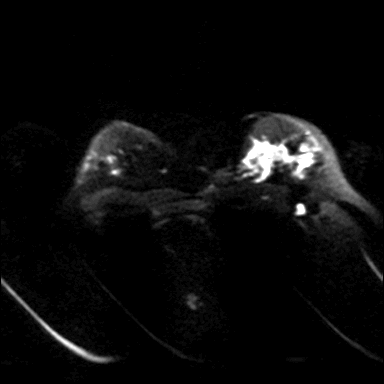
Breast MRI, one axial slice; position 30 of 36 along the scan axis; diffusion-weighted series; image 2 of 4 stored at this slice position (different b-values; order by instance number); 3 T; 4 mm slice thickness; 384 × 384 image matrix. Female patient.
Structures marked on this image (manually delineated by an expert):
- tumour on diffusion-weighted imaging: bounding box <256,145,312,165> (left, top, right, bottom; pixels)